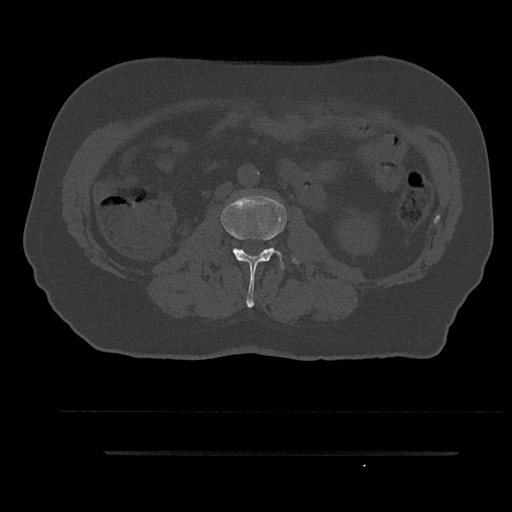
CT including the spine, one axial slice; position 97 of 797 along the scan axis; reconstruction kernel Br40s/3; bone window (W 1800 / L 400 HU); 0.5 mm slice thickness; 512 × 512 image matrix. Male patient, age 63 years. From the clinical record (not read from this slice): primary cancer: renal.
Structures marked on this image (semi-automatic segmentation, software-assisted and operator-edited):
- L2 vertebra: bounding box (x1, y1, x2, y2) in pixels: (221, 195, 299, 308)